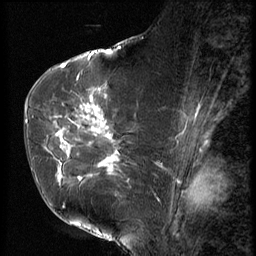
Breast MRI (dynamic contrast-enhanced), one sagittal slice. Position 34 of 56 along the scan axis. 3 images stored at this slice position (order not interpretable as contrast timing). 1.5 T. TE 4.2 ms, TR 9 ms. 2.5 mm slice thickness. 256 × 256 image matrix, field of view 180 × 180 mm. Female patient, age 61 years. Case-level facts recorded for this patient, not image findings: setting: breast cancer imaged before/during neoadjuvant chemotherapy; receptor status: HR-positive, HER2-negative.
Structures marked on this image (semi-automatically segmented with operator editing):
- analysis volume of interest (the breast-tissue region the enhancement analysis was run in; not a lesion): box from (x=47, y=89) to (x=153, y=191) px
- tumour enhancement mask (voxels above the 140 % enhancement threshold inside the analysis volume of interest): (x=55, y=89)–(x=116, y=180)